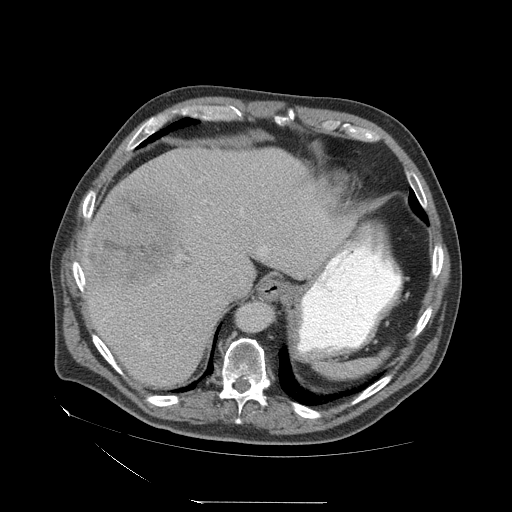
Contrast-enhanced abdominal CT (liver protocol), one axial slice; slice 52 of 83 in the series (ordered by position); reconstruction kernel STANDARD; 140 kVp; soft-tissue window (W 400 / L 40 HU); 512 × 512 image matrix, field of view 460 × 460 mm. Case-level facts recorded for this patient, not image findings: diagnosis: hepatocellular carcinoma (patient treated with transarterial chemoembolisation; whether this scan precedes or follows treatment is not stated here); TNM stage (as recorded): Stage-I; Child-Pugh class: A; tumour differentiation: well differentiated.
Structures marked on this image (semi-automatic segmentation, software-assisted and operator-edited):
- liver parenchyma outside the tumour (the mass and vessels are separate outlines, so this box may not span the whole liver): box from (x=82, y=148) to (x=354, y=388) px
- mass: (x=87, y=190)–(x=180, y=293)
- liver vessels: (x=241, y=209)–(x=263, y=251)